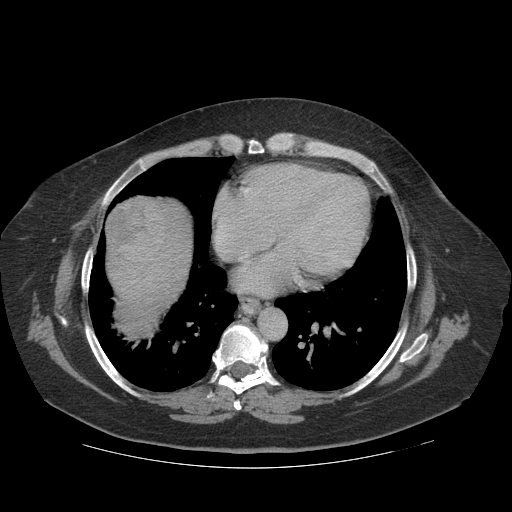
Contrast-enhanced abdominal CT (liver protocol), one axial slice. Slice 108 of 121 in the series (ordered by position). 140 kVp. Soft-tissue window (W 400 / L 40 HU). 2.5 mm slice thickness. 512 × 512 image matrix, field of view 420 × 420 mm. From the clinical record (not read from this slice): diagnosis: hepatocellular carcinoma (patient treated with transarterial chemoembolisation; whether this scan precedes or follows treatment is not stated here); TNM stage (as recorded): Stage-IIIA; Child-Pugh class: A; tumour differentiation: well differentiated; tumour nodularity: multinodular.
Outlined on this slice (semi-automatically segmented with operator editing):
- liver parenchyma outside the tumour (the mass and vessels are separate outlines, so this box may not span the whole liver): bounding box (x1, y1, x2, y2) in pixels: (106, 196, 191, 320)
- mass: (106, 200, 146, 251)